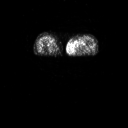
FDG PET of an extremity soft-tissue mass (from a PET/CT study), one axial slice; position 10 of 91 along the scan axis; 3.27 mm slice thickness; 128 × 128 image matrix, field of view 700 × 700 mm. Female patient, age 74 years. Case-level facts recorded for this patient, not image findings: histological type: pleomorphic leiomyosarcoma; grade: high; site of the primary tumour: left thigh.
Outlined on this slice (expert contour drawn on MRI and transferred to this co-registered scan by the dataset authors):
- gross tumour volume including surrounding oedema: bounding box [x1, y1, x2, y2] px = [71, 38, 87, 51]